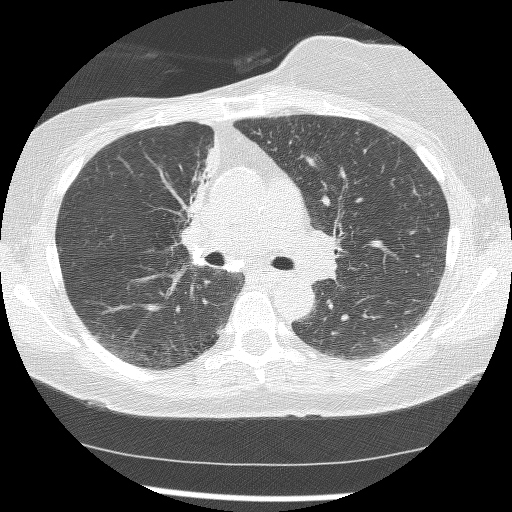
Chest CT (low-dose screening protocol), one axial image. Baseline screening round. Lung window (W 1500 / L -600 HU). 2.5 mm slice thickness. Lung (sharp) reconstruction kernel (BONE). Slice 62 of 172 in the series. Female, age 56 years at enrolment. Current smoker at enrolment.
Expert reader's lesion annotation, bounding box <161,143,216,256> (left, top, right, bottom; pixels). The screening reader recorded 2 non-calcified nodules or masses ≥4 mm on this exam (right lower lobe, right middle lobe); which of them this box marks is not recorded. Participant outcome: lung cancer diagnosed 1185 days after this screen (after the third annual screen) — adenocarcinoma, NOS, right upper lobe, stage IIIB (AJCC 6th edition), 8 mm at pathology.